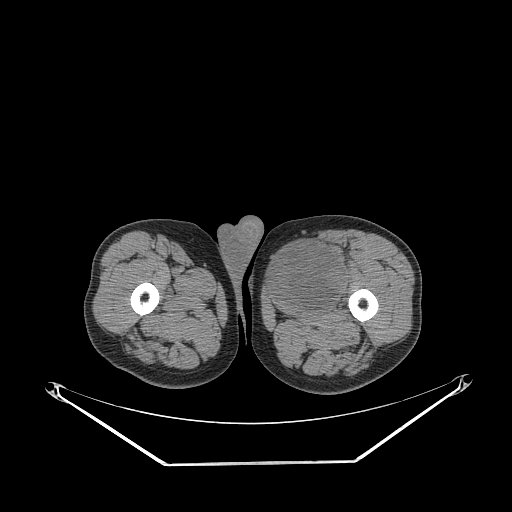
CT of an extremity soft-tissue mass (from a PET/CT study), one axial slice. 140 kVp. Soft-tissue window (W 400 / L 40 HU). 3.75 mm slice thickness. 512 × 512 image matrix, field of view 500 × 500 mm. Male patient. Case-level facts recorded for this patient, not image findings: histological type: pleiomorphic liposarcoma; grade: high; site of the primary tumour: left thigh.
Annotated regions visible in this slice (expert contour drawn on MRI and transferred to this co-registered scan by the dataset authors):
- gross tumour volume including surrounding oedema: bounding box (x1, y1, x2, y2) in pixels: (270, 237, 350, 305)
- gross tumour volume (mass): (270, 242, 346, 305)